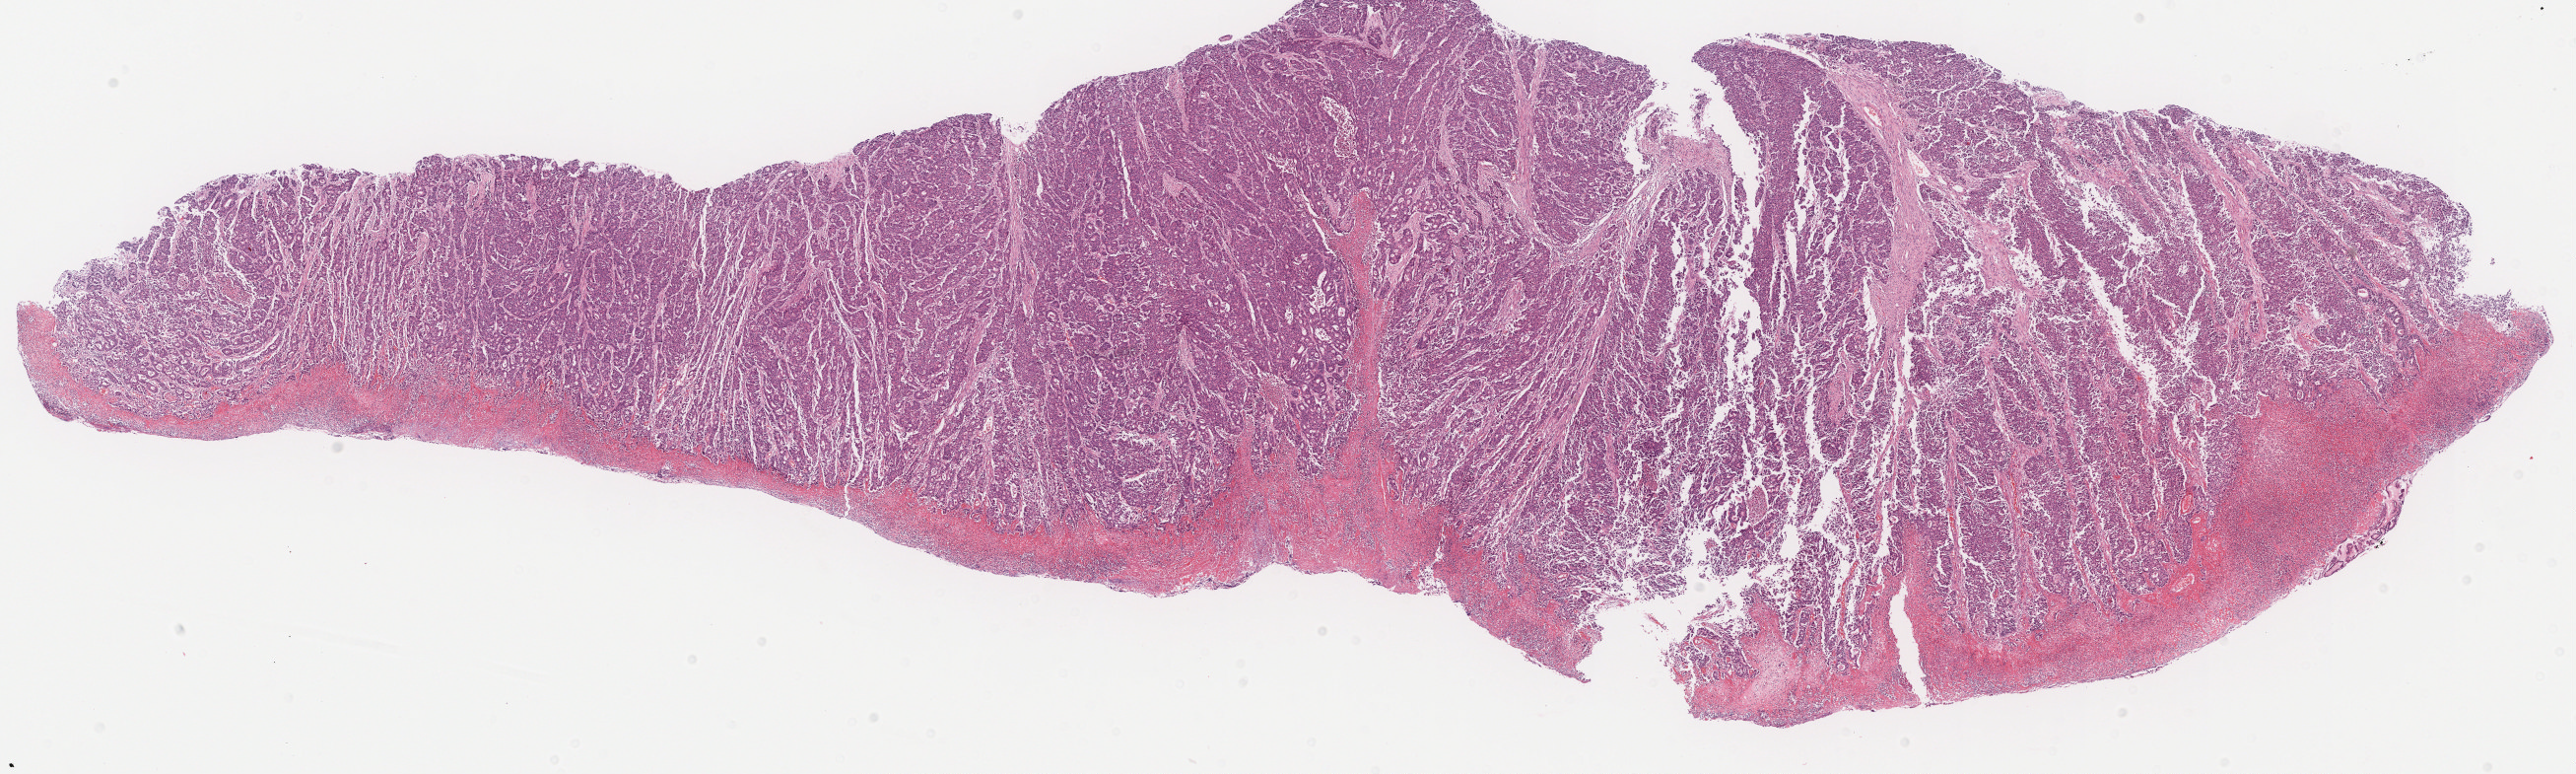
Digitized H&E-stained tissue section (whole slide), whole scanned area (about 20.7 x 6.2 mm, slide scanned at 20x) shown as a low-resolution overview, formalin-fixed paraffin-embedded (FFPE) diagnostic section, sample: primary tumour, stomach. Male, age 73 years at initial diagnosis. Histologic grade: G3 (poorly differentiated).
• lymph nodes positive (case pathology): 2 of 48 examined
• histologic diagnosis: Carcinoma, diffuse type (gastric antrum)
• AJCC pathologic stage: IIB